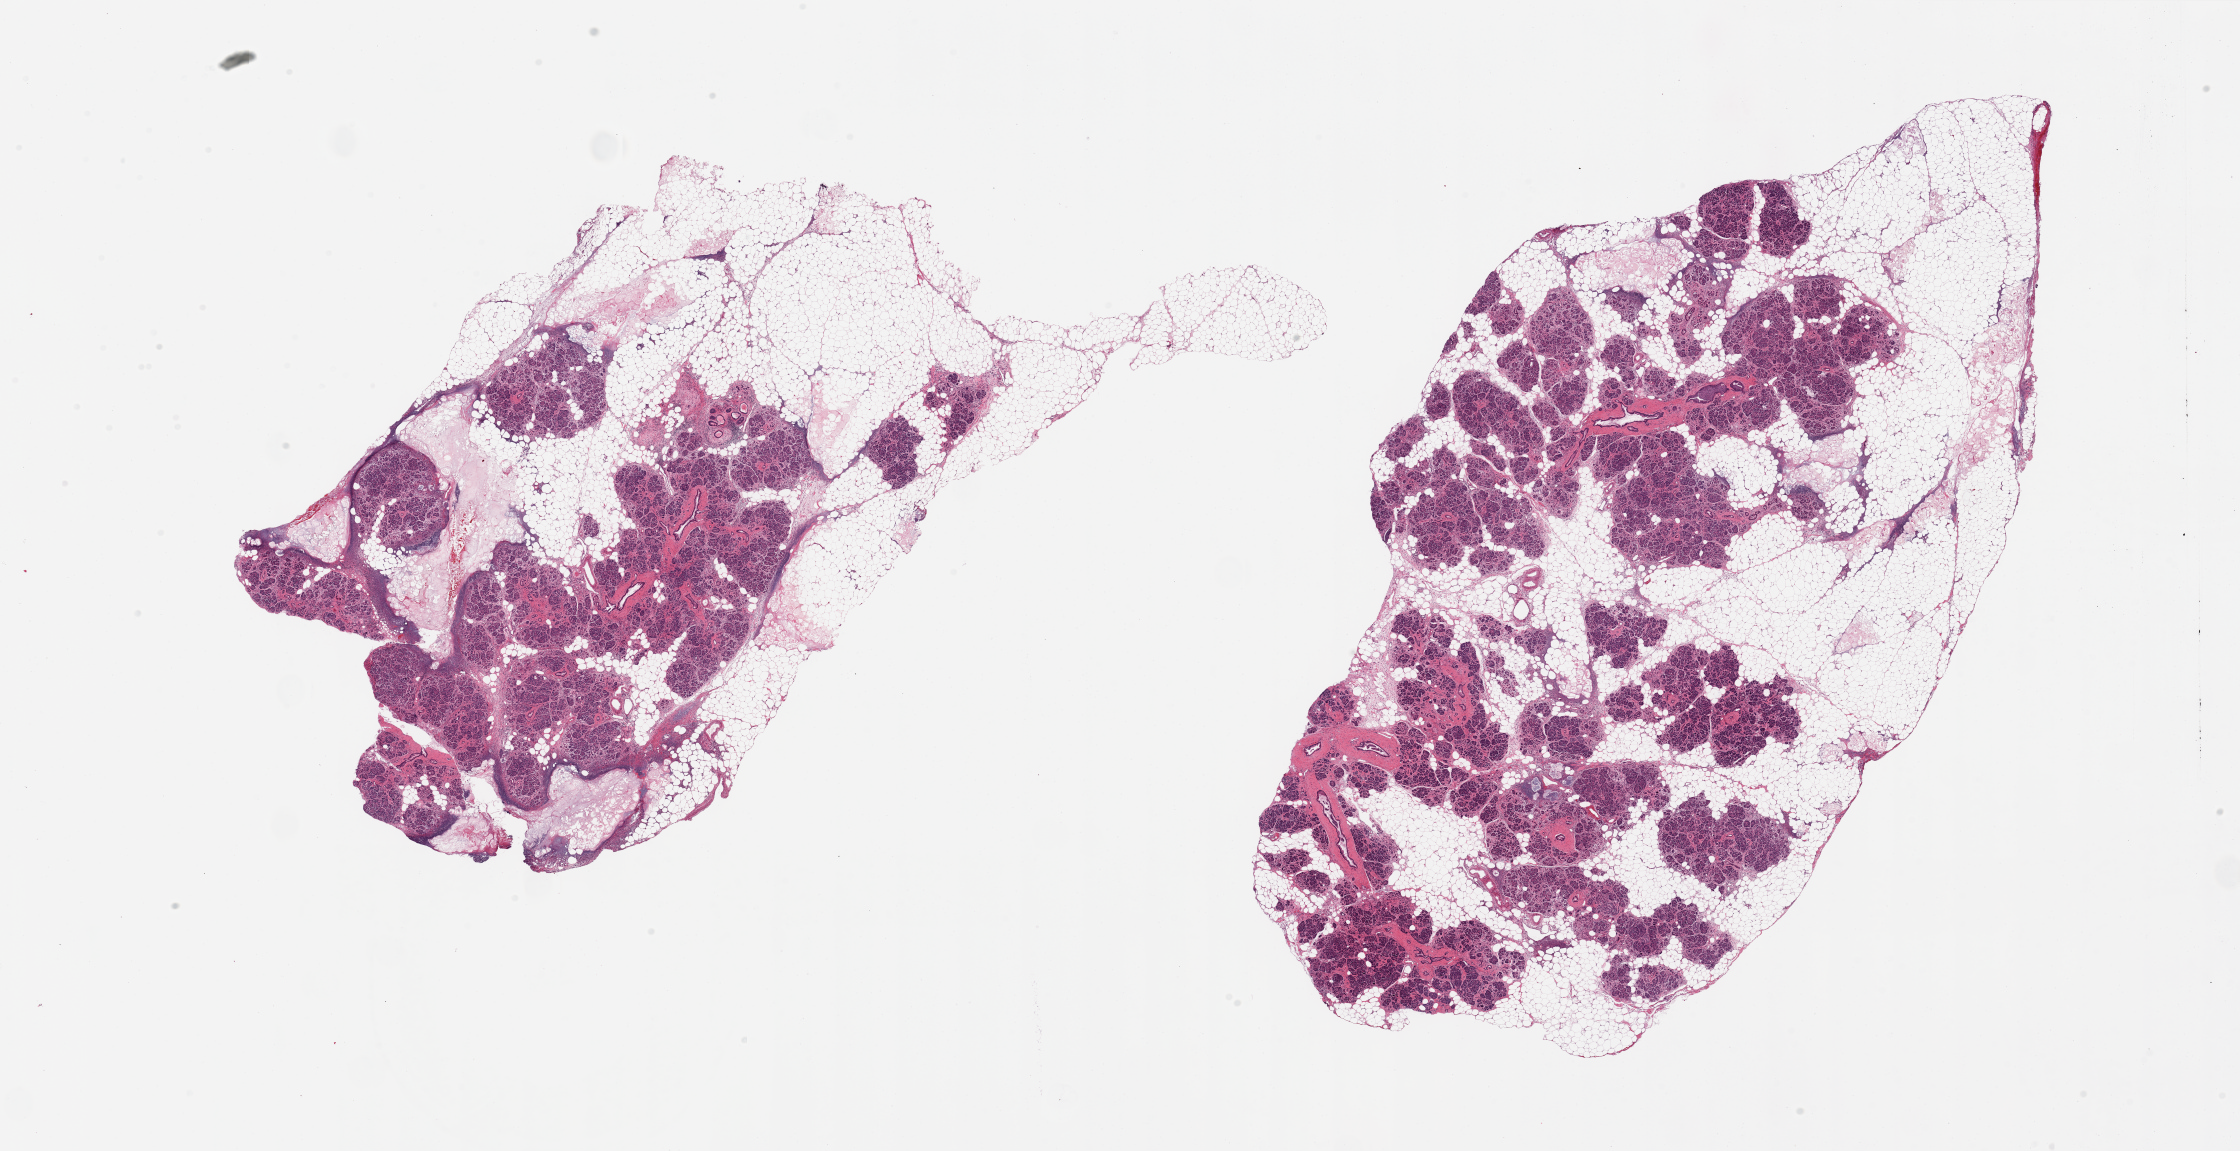
Digitized H&E-stained section, brightfield, whole scanned area (about 35.4 x 18.2 mm, acquisition: 20x scan) shown as a low-resolution overview, PAXgene-fixed paraffin-embedded (PFPE) section, target tissue: pancreas, donor tissue sample. Female donor.
Pathologist's review note for this sample: 2 pieces, 18x9 & 18x10mm; extensive pancreatitis, saponification, ductal squamous metaplasia, areas and ensqaured; Antemortem changes with inflammatory response.